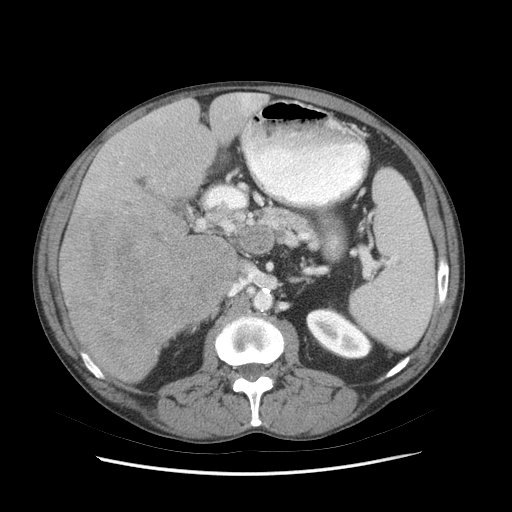
Contrast-enhanced abdominal CT (liver protocol), one axial slice; position 37 of 89 along the scan axis; reconstruction kernel STANDARD; 140 kVp; soft-tissue window (W 400 / L 40 HU); 2.5 mm slice thickness; 512 × 512 image matrix, field of view 380 × 380 mm. Case-level facts recorded for this patient, not image findings: diagnosis: hepatocellular carcinoma (patient treated with transarterial chemoembolisation; whether this scan precedes or follows treatment is not stated here); TNM stage (as recorded): Stage-IIIB; Child-Pugh class: A; tumour differentiation: moderately differentiated; tumour nodularity: multinodular.
Structures marked on this image (semi-automatically segmented with operator editing):
- liver parenchyma outside the tumour (the mass and vessels are separate outlines, so this box may not span the whole liver): bounding box [x1, y1, x2, y2] px = [58, 92, 268, 382]
- mass: [60, 206, 235, 381]
- liver vessels: [121, 94, 256, 164]